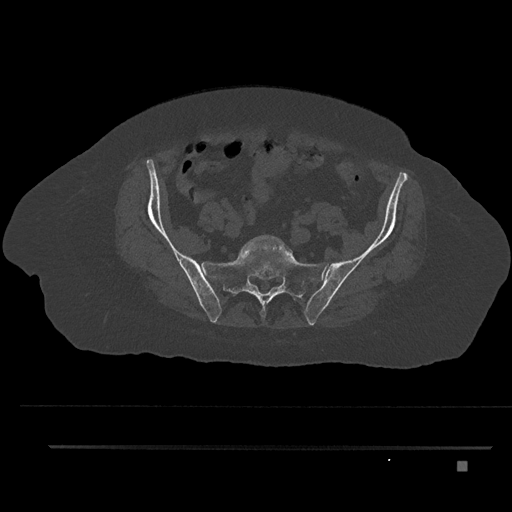
CT including the spine, one axial slice. Slice 1 of 797 in the series (ordered by position). Reconstruction kernel Br40s/3. Bone window (W 1800 / L 400 HU). 0.5 mm slice thickness. 512 × 512 image matrix, field of view 437 × 437 mm. Patient: female, 76 years. Case-level facts recorded for this patient, not image findings: primary cancer: lung.
Outlined on this slice (semi-automatic segmentation, software-assisted and operator-edited):
- L5 vertebra: bounding box [x1, y1, x2, y2] px = [242, 235, 294, 260]